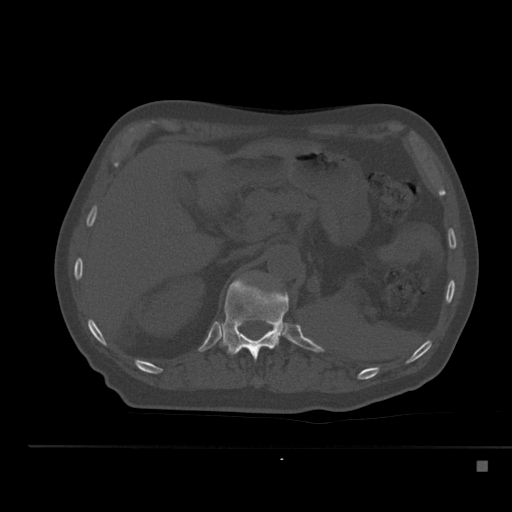
CT including the spine, one axial slice. Slice 228 of 517 in the series (ordered by position). Reconstruction kernel Br40s. Bone window (W 1800 / L 400 HU). 512 × 512 image matrix, field of view 408 × 408 mm. Patient: male, 70 years. From the clinical record (not read from this slice): primary cancer: renal; vertebrae with lytic lesions (as recorded): T4, T6, T10, T12, L3, L4, L5.
Structures marked on this image (semi-automatic segmentation, software-assisted and operator-edited):
- T12 vertebra: box from (x=220, y=278) to (x=289, y=360) px